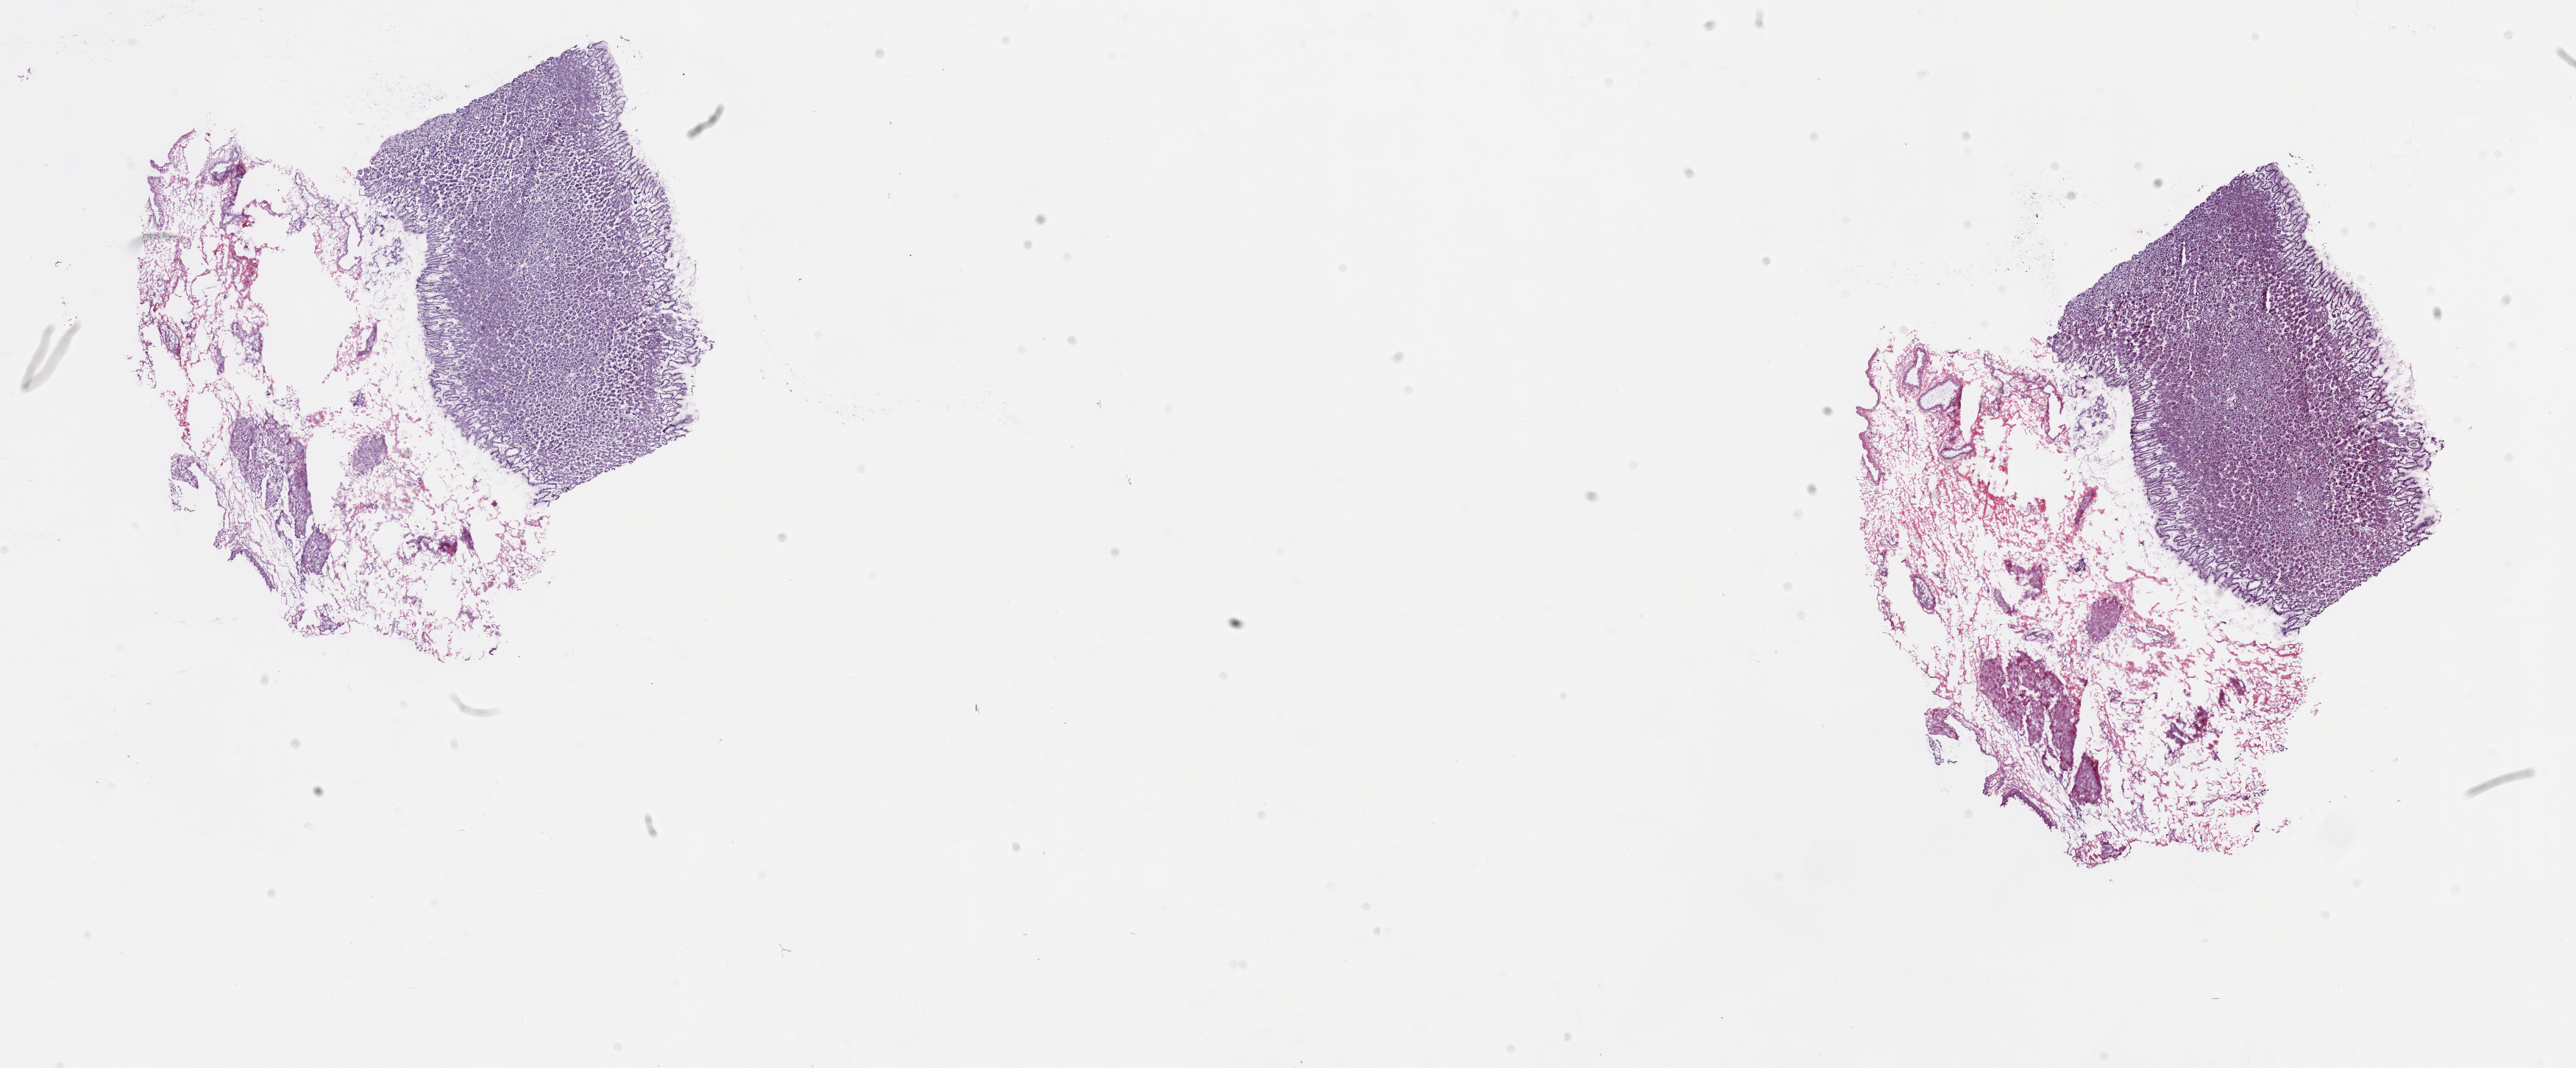
Whole-slide histology image, H&E, low-resolution overview of the scanned area, about 27.8 x 11.5 mm (slide scanned at 20x); frozen section; esophagus, solid tissue normal (non-tumour tissue) sample. Male, age 56 years at initial diagnosis. Composition of this section per pathologist review: tumour cells 0%, tumour nuclei 0%, normal cells 100%, stromal cells 0%, necrosis 0%. Infiltration values recorded for this section: lymphocyte infiltration 0%, monocyte infiltration 0%, neutrophil infiltration 0%.
- this section: solid tissue normal (non-tumour) sample from the same patient
- patient diagnosis: Adenocarcinoma, NOS (lower third of esophagus)